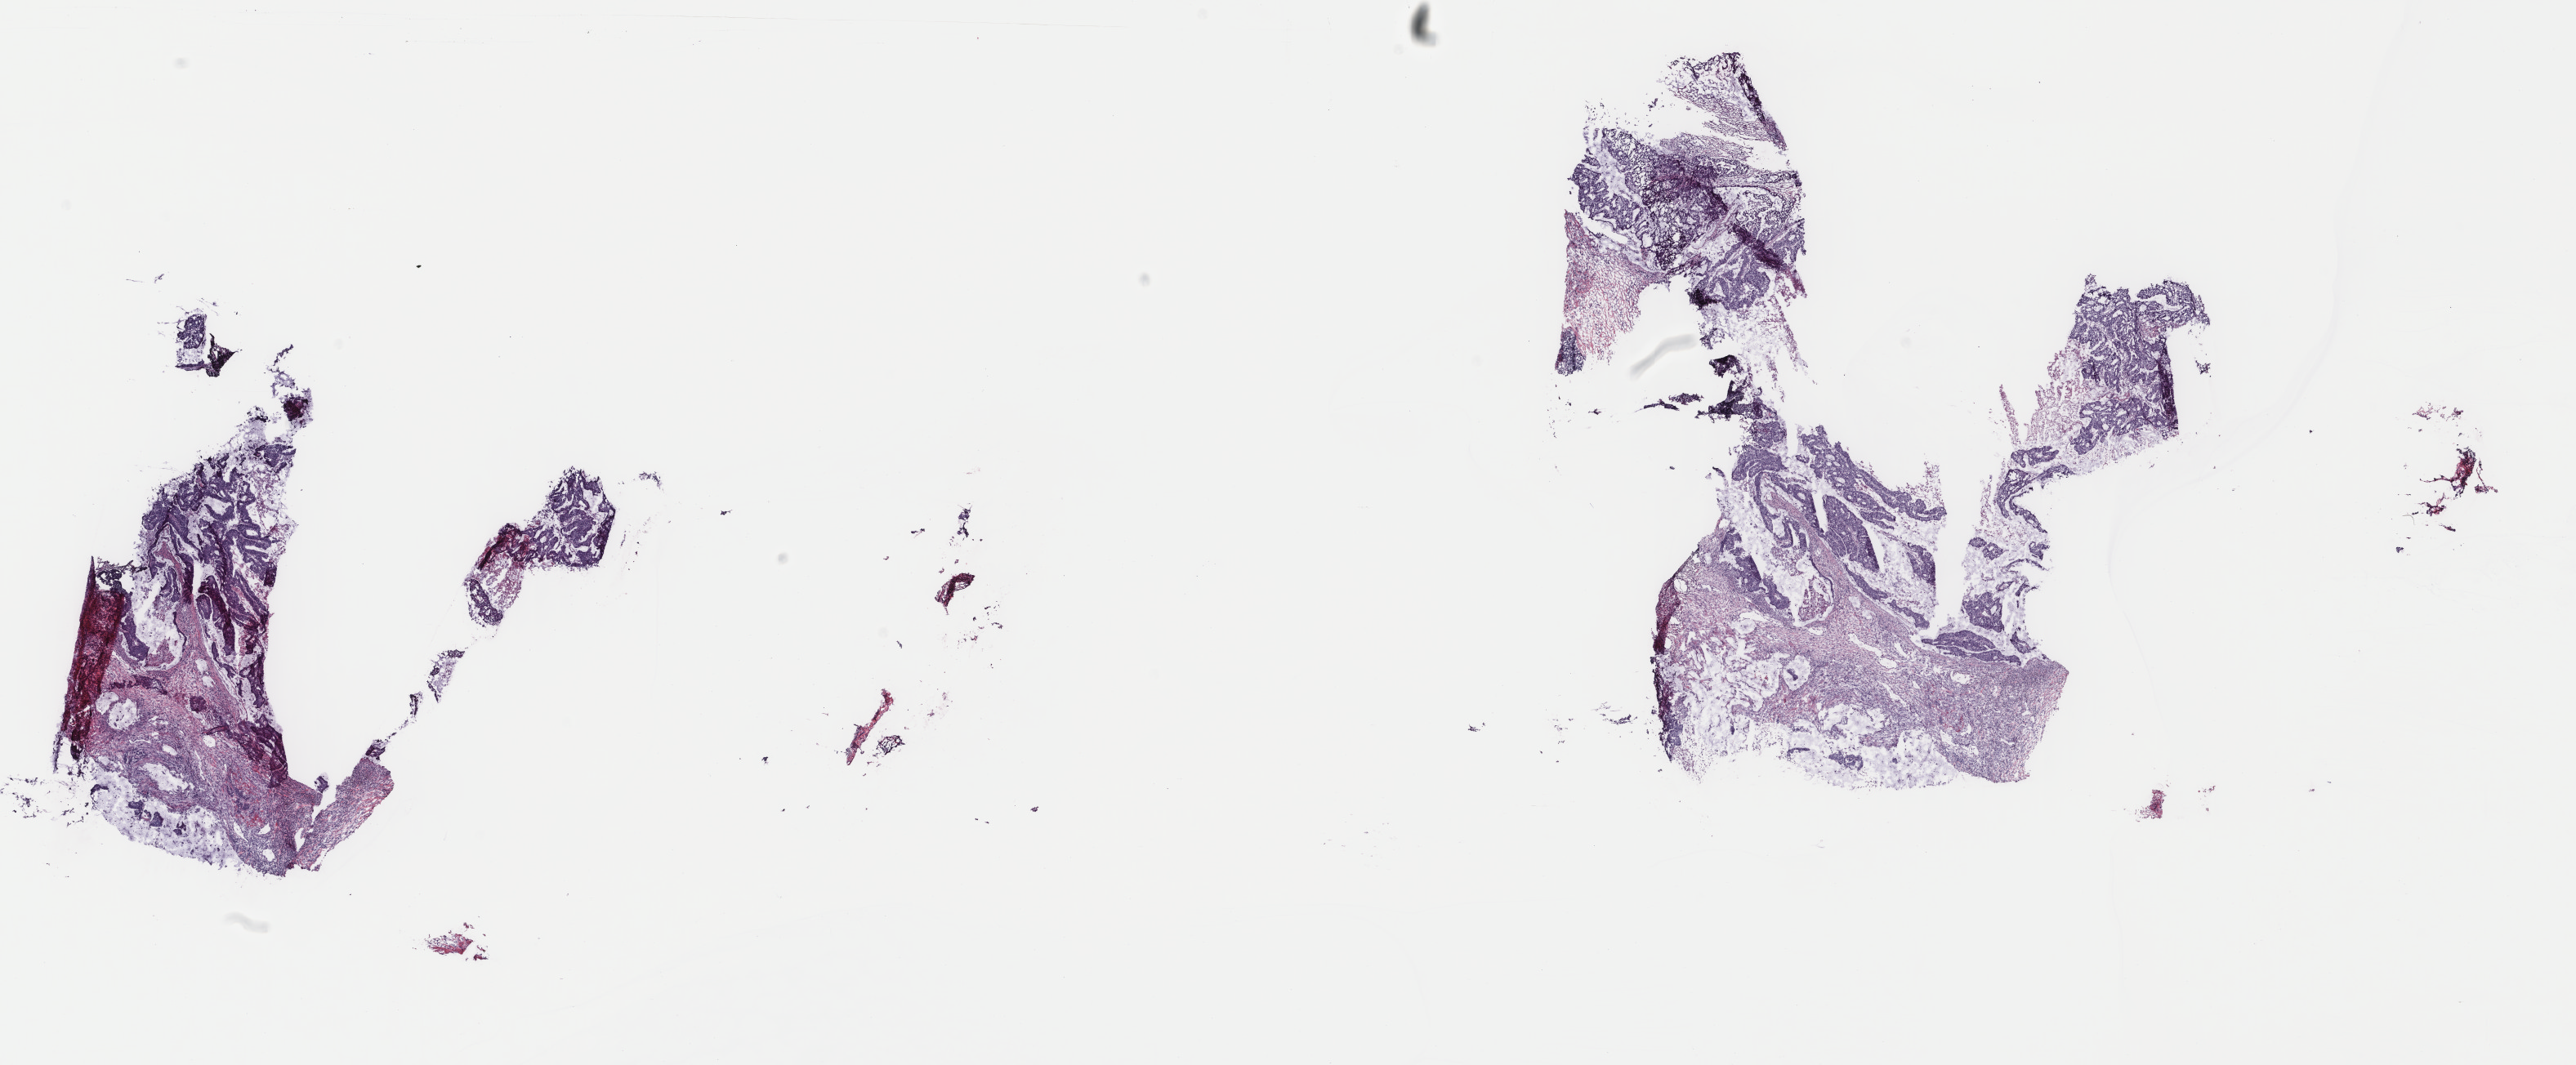
Whole-slide histology image, H&E-stained — shown as a low-resolution overview of the whole scanned area (about 25.0 x 10.4 mm, slide scanned at 40x), frozen section, primary tumour sample from the colon. Female patient. Composition of this section per pathologist review: tumour cells 70%, tumour nuclei 70%, normal cells 0%, stromal cells 26%, necrosis 4%. Infiltration values recorded for this section: lymphocyte infiltration 5%, monocyte infiltration 3%, neutrophil infiltration 6%.
AJCC pathologic stage: IIA (7th edition). Histologic diagnosis: Adenocarcinoma, NOS (transverse colon).